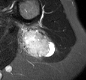
MRI of an extremity soft-tissue mass, one axial slice. Position 13 of 30 along the scan axis. STIR. MR volume resampled by the dataset authors to the PET/CT grid (not the native acquisition matrix). 86 × 80 image matrix, field of view 84 × 78 mm. Female patient. Case-level facts recorded for this patient, not image findings: histological type: malignant fibrous histiocytoma; grade: low; site of the primary tumour: left arm.
Outlined on this slice (expert contour drawn on MRI and transferred to this co-registered scan by the dataset authors):
- gross tumour volume (mass): bounding box <17,24,55,59> (left, top, right, bottom; pixels)